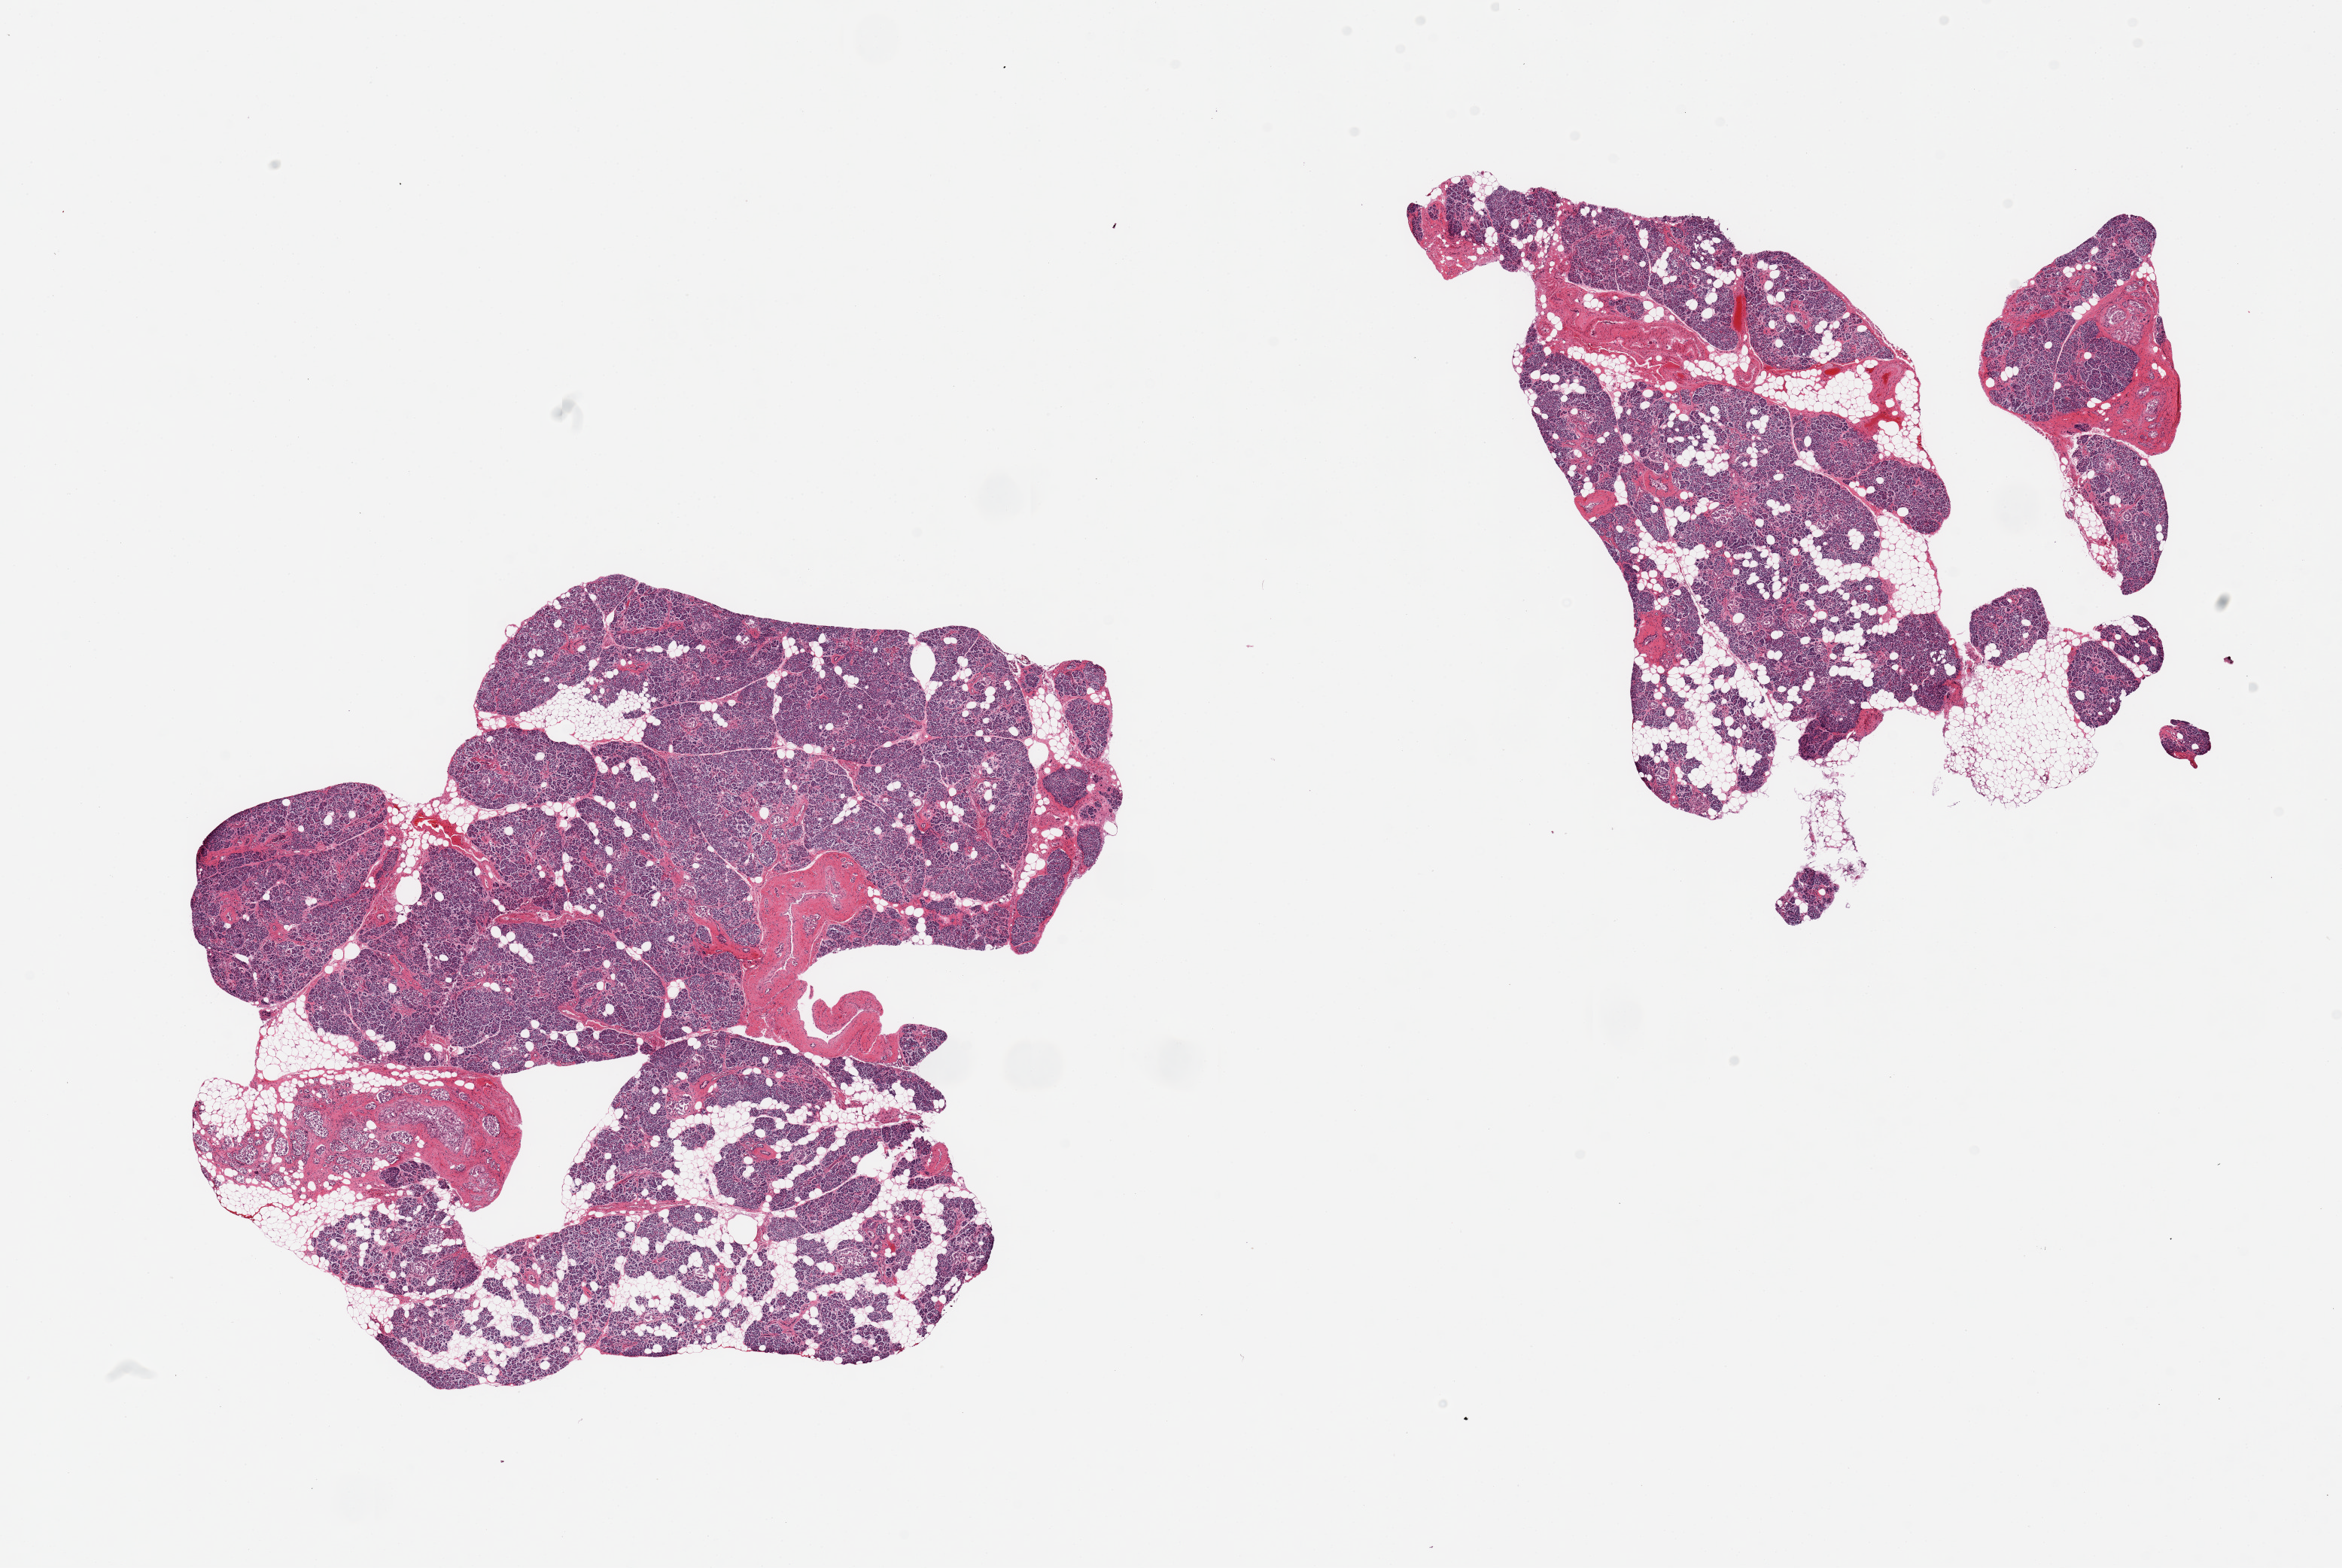
Digitized hematoxylin and eosin (H&E)-stained section — whole scanned area (about 24.6 x 16.5 mm) shown as a low-resolution overview, PAXgene-fixed paraffin-embedded (PFPE) section, target tissue: pancreas, donor tissue sample.
• pathologist's review note for this sample: 2 pieces, ~10-20% interstitial fat; Islets poorly visualized; moderate-marked saponification/autolysis